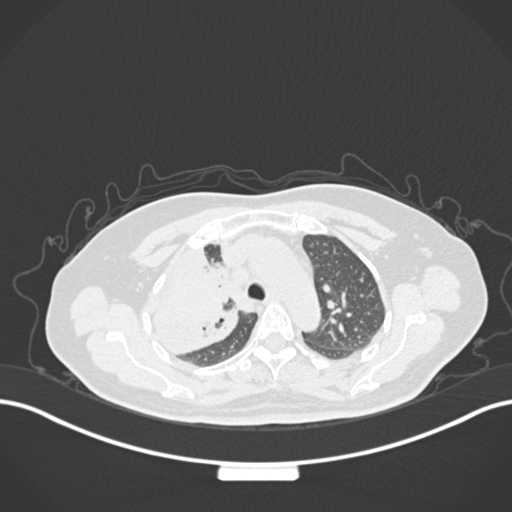
Chest CT, one axial slice; slice 116 of 177 in the series (ordered by position); reconstruction kernel B30f; 120 kVp; lung window (W 1500 / L -600 HU); 1 mm slice thickness; 512 × 512 image matrix, field of view 400 × 400 mm. Female patient, age 60 years. Case-level facts recorded for this patient, not image findings: clinical TNM (as recorded): T3 N1 M1.
Outlined on this slice (bounding box drawn by a radiologist):
- lung tumour (recorded histology: adenocarcinoma): bounding box (x1, y1, x2, y2) in pixels: (151, 242, 240, 352)